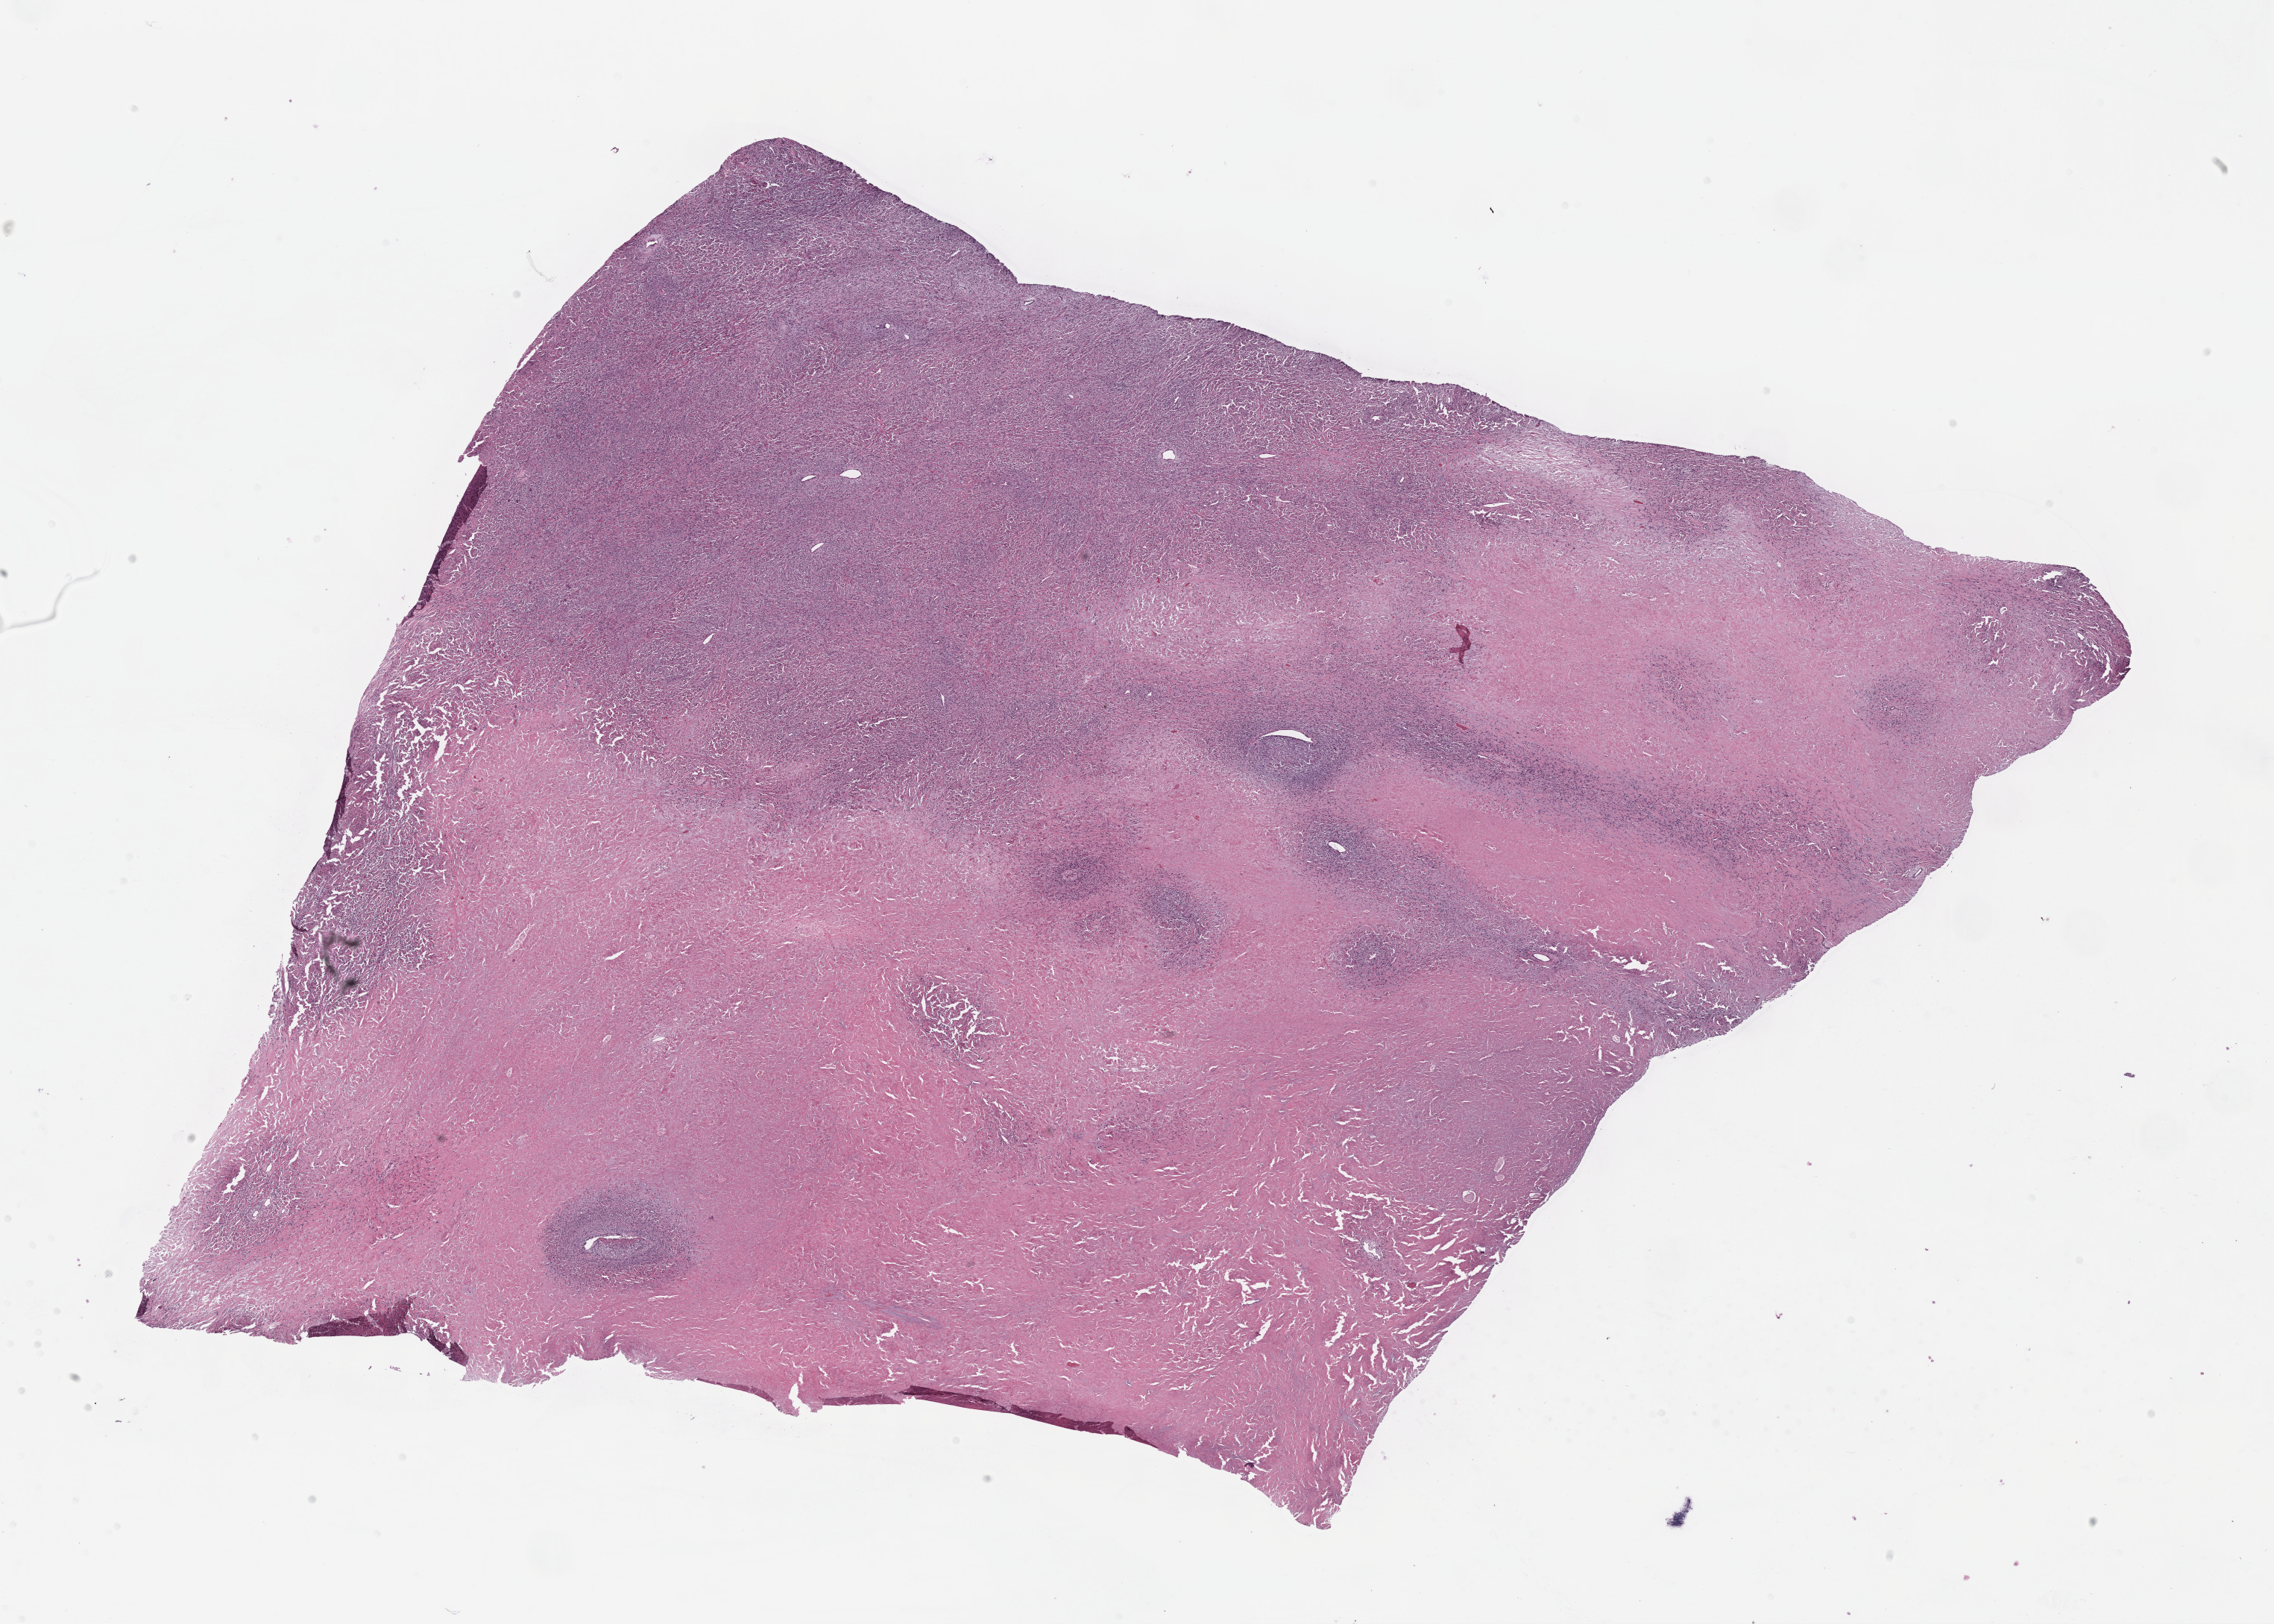
Whole-slide histology image, Hematoxylin and eosin (H&E) stained, a low-resolution overview of the entire scanned area, about 24.7 x 17.6 mm (acquisition: 40x scan). Formalin-fixed paraffin-embedded (FFPE) diagnostic section. Primary tumour sample from the connective, subcutaneous and other soft tissues. Female, age 20 years at initial diagnosis.
- histologic diagnosis: Malignant peripheral nerve sheath tumor (connective, subcutaneous and other soft tissues of lower limb and hip)